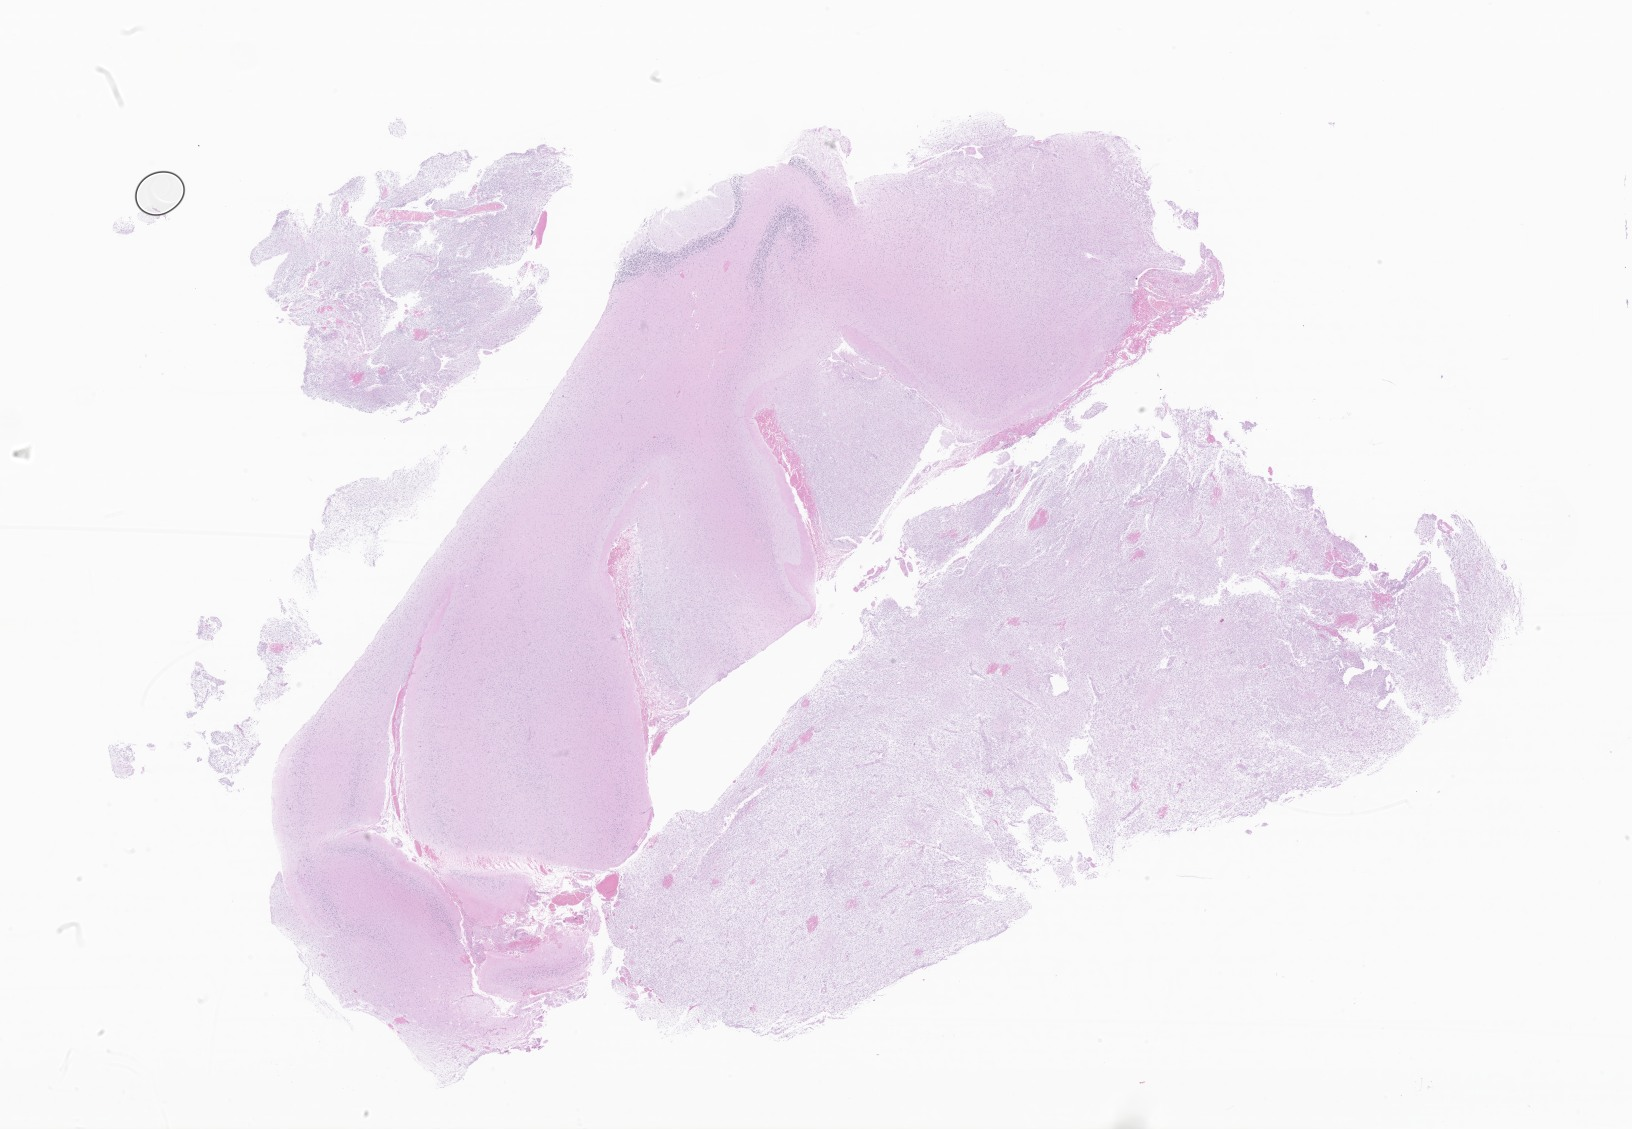
Digitized haematoxylin and eosin-stained section of tumor tissue from the brain, shown as a low-resolution overview of the whole scanned area (about 27.5 x 19.0 mm), formalin-fixed paraffin-embedded section. Patient female; age 45 months (3 years 9 months).
• recorded diagnosis: Neoplasm, uncertain whether benign or malignant